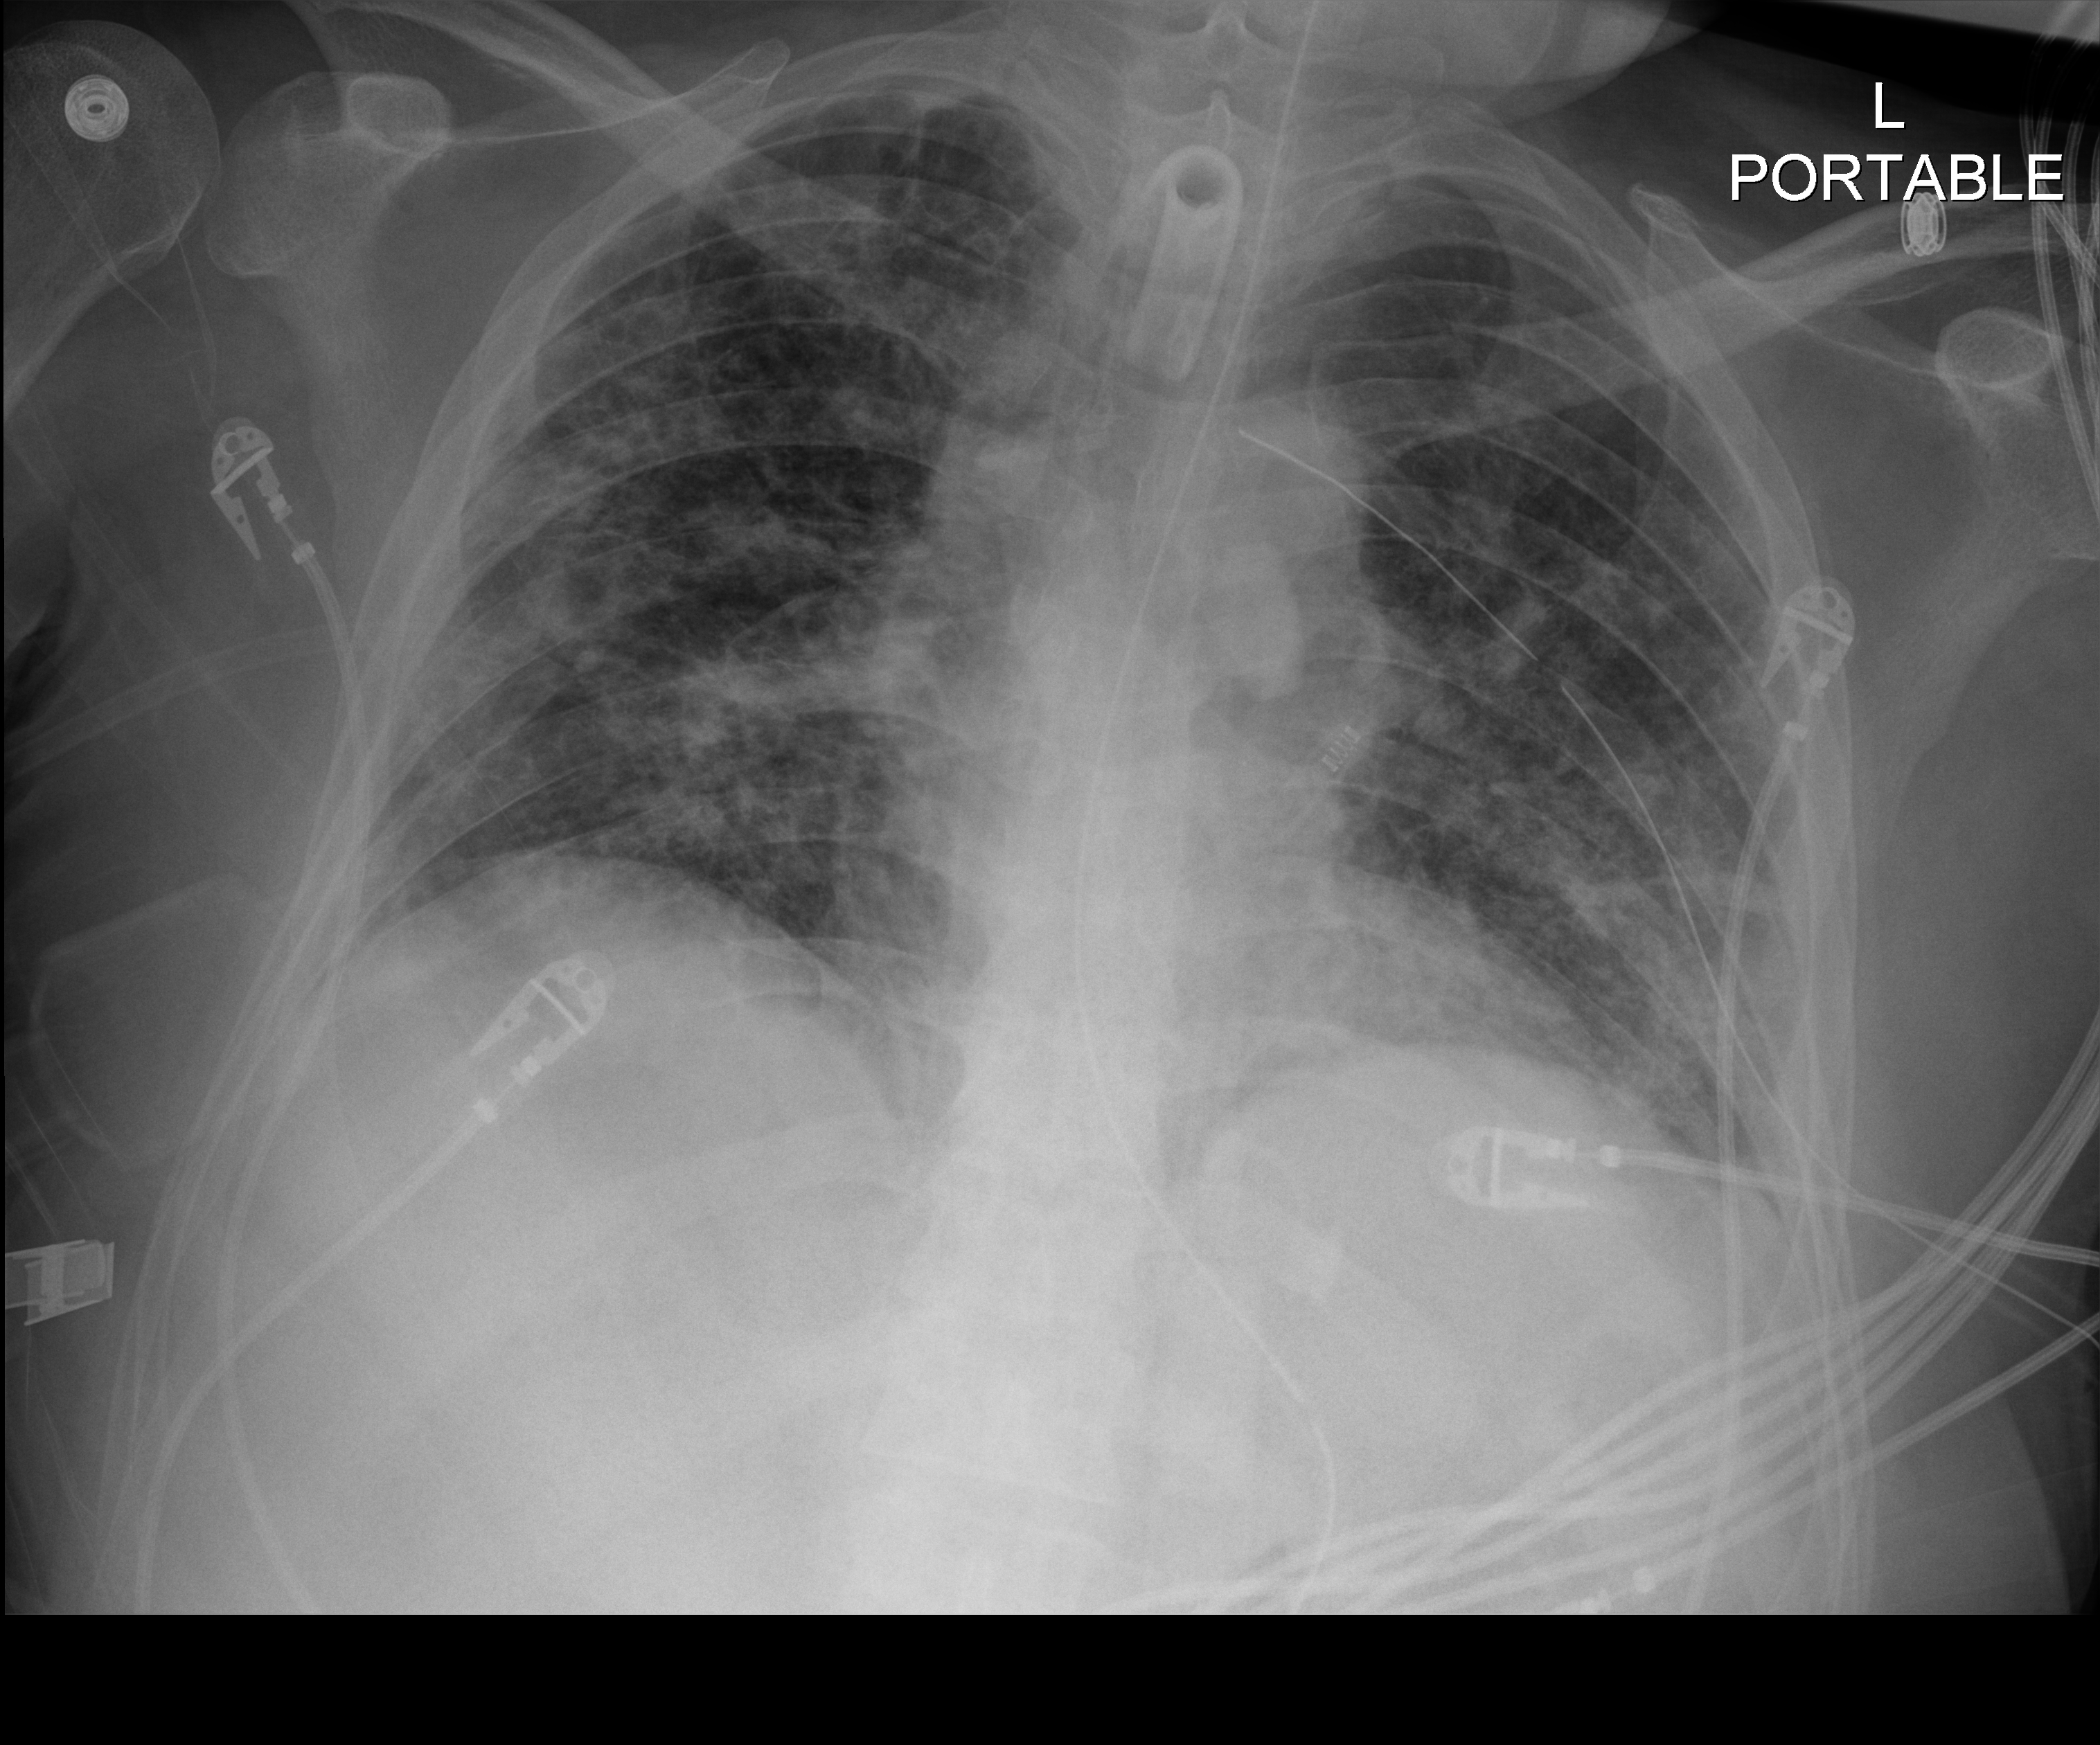
Portable chest radiograph; anteroposterior (AP) projection. Male patient hospitalised with COVID-19, age 18–59 years.
Admission-level facts for this patient (not findings on this image; timing relative to this image not recorded):
- mechanically ventilated during this hospital stay: yes